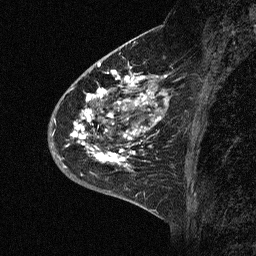
Breast MRI (dynamic contrast-enhanced), one sagittal slice. Slice 22 of 64 in the series (ordered by position). Dynamic contrast-enhanced study with each time point stored as its own series, time point 2 of 3 at this slice position (early post-contrast, ordered by acquisition time). 1.5 T. TE 4.5 ms, TR 11 ms. 256 × 256 image matrix, field of view 200 × 200 mm. Female patient, age 46 years. Case-level facts recorded for this patient, not image findings: setting: breast cancer imaged before/during neoadjuvant chemotherapy; receptor status: HER2-positive.
Structures marked on this image (semi-automatically segmented with operator editing):
- analysis volume of interest (the breast-tissue region the enhancement analysis was run in; not a lesion): box from (x=43, y=72) to (x=176, y=177) px
- tumour enhancement mask (voxels above the 90 % enhancement threshold inside the analysis volume of interest): (x=71, y=72)–(x=167, y=167)